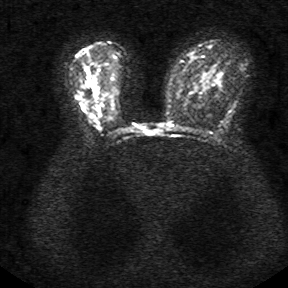
Breast MRI, one axial slice; slice 20 of 34 in the series (ordered by position); diffusion-weighted series; image 2 of 4 stored at this slice position (different b-values; order by instance number); 1.5 T; 288 × 288 image matrix. Female patient.
Annotated regions visible in this slice (outlined manually by an expert reader):
- tumour on diffusion-weighted imaging: bounding box (x1, y1, x2, y2) in pixels: (86, 78, 96, 88)